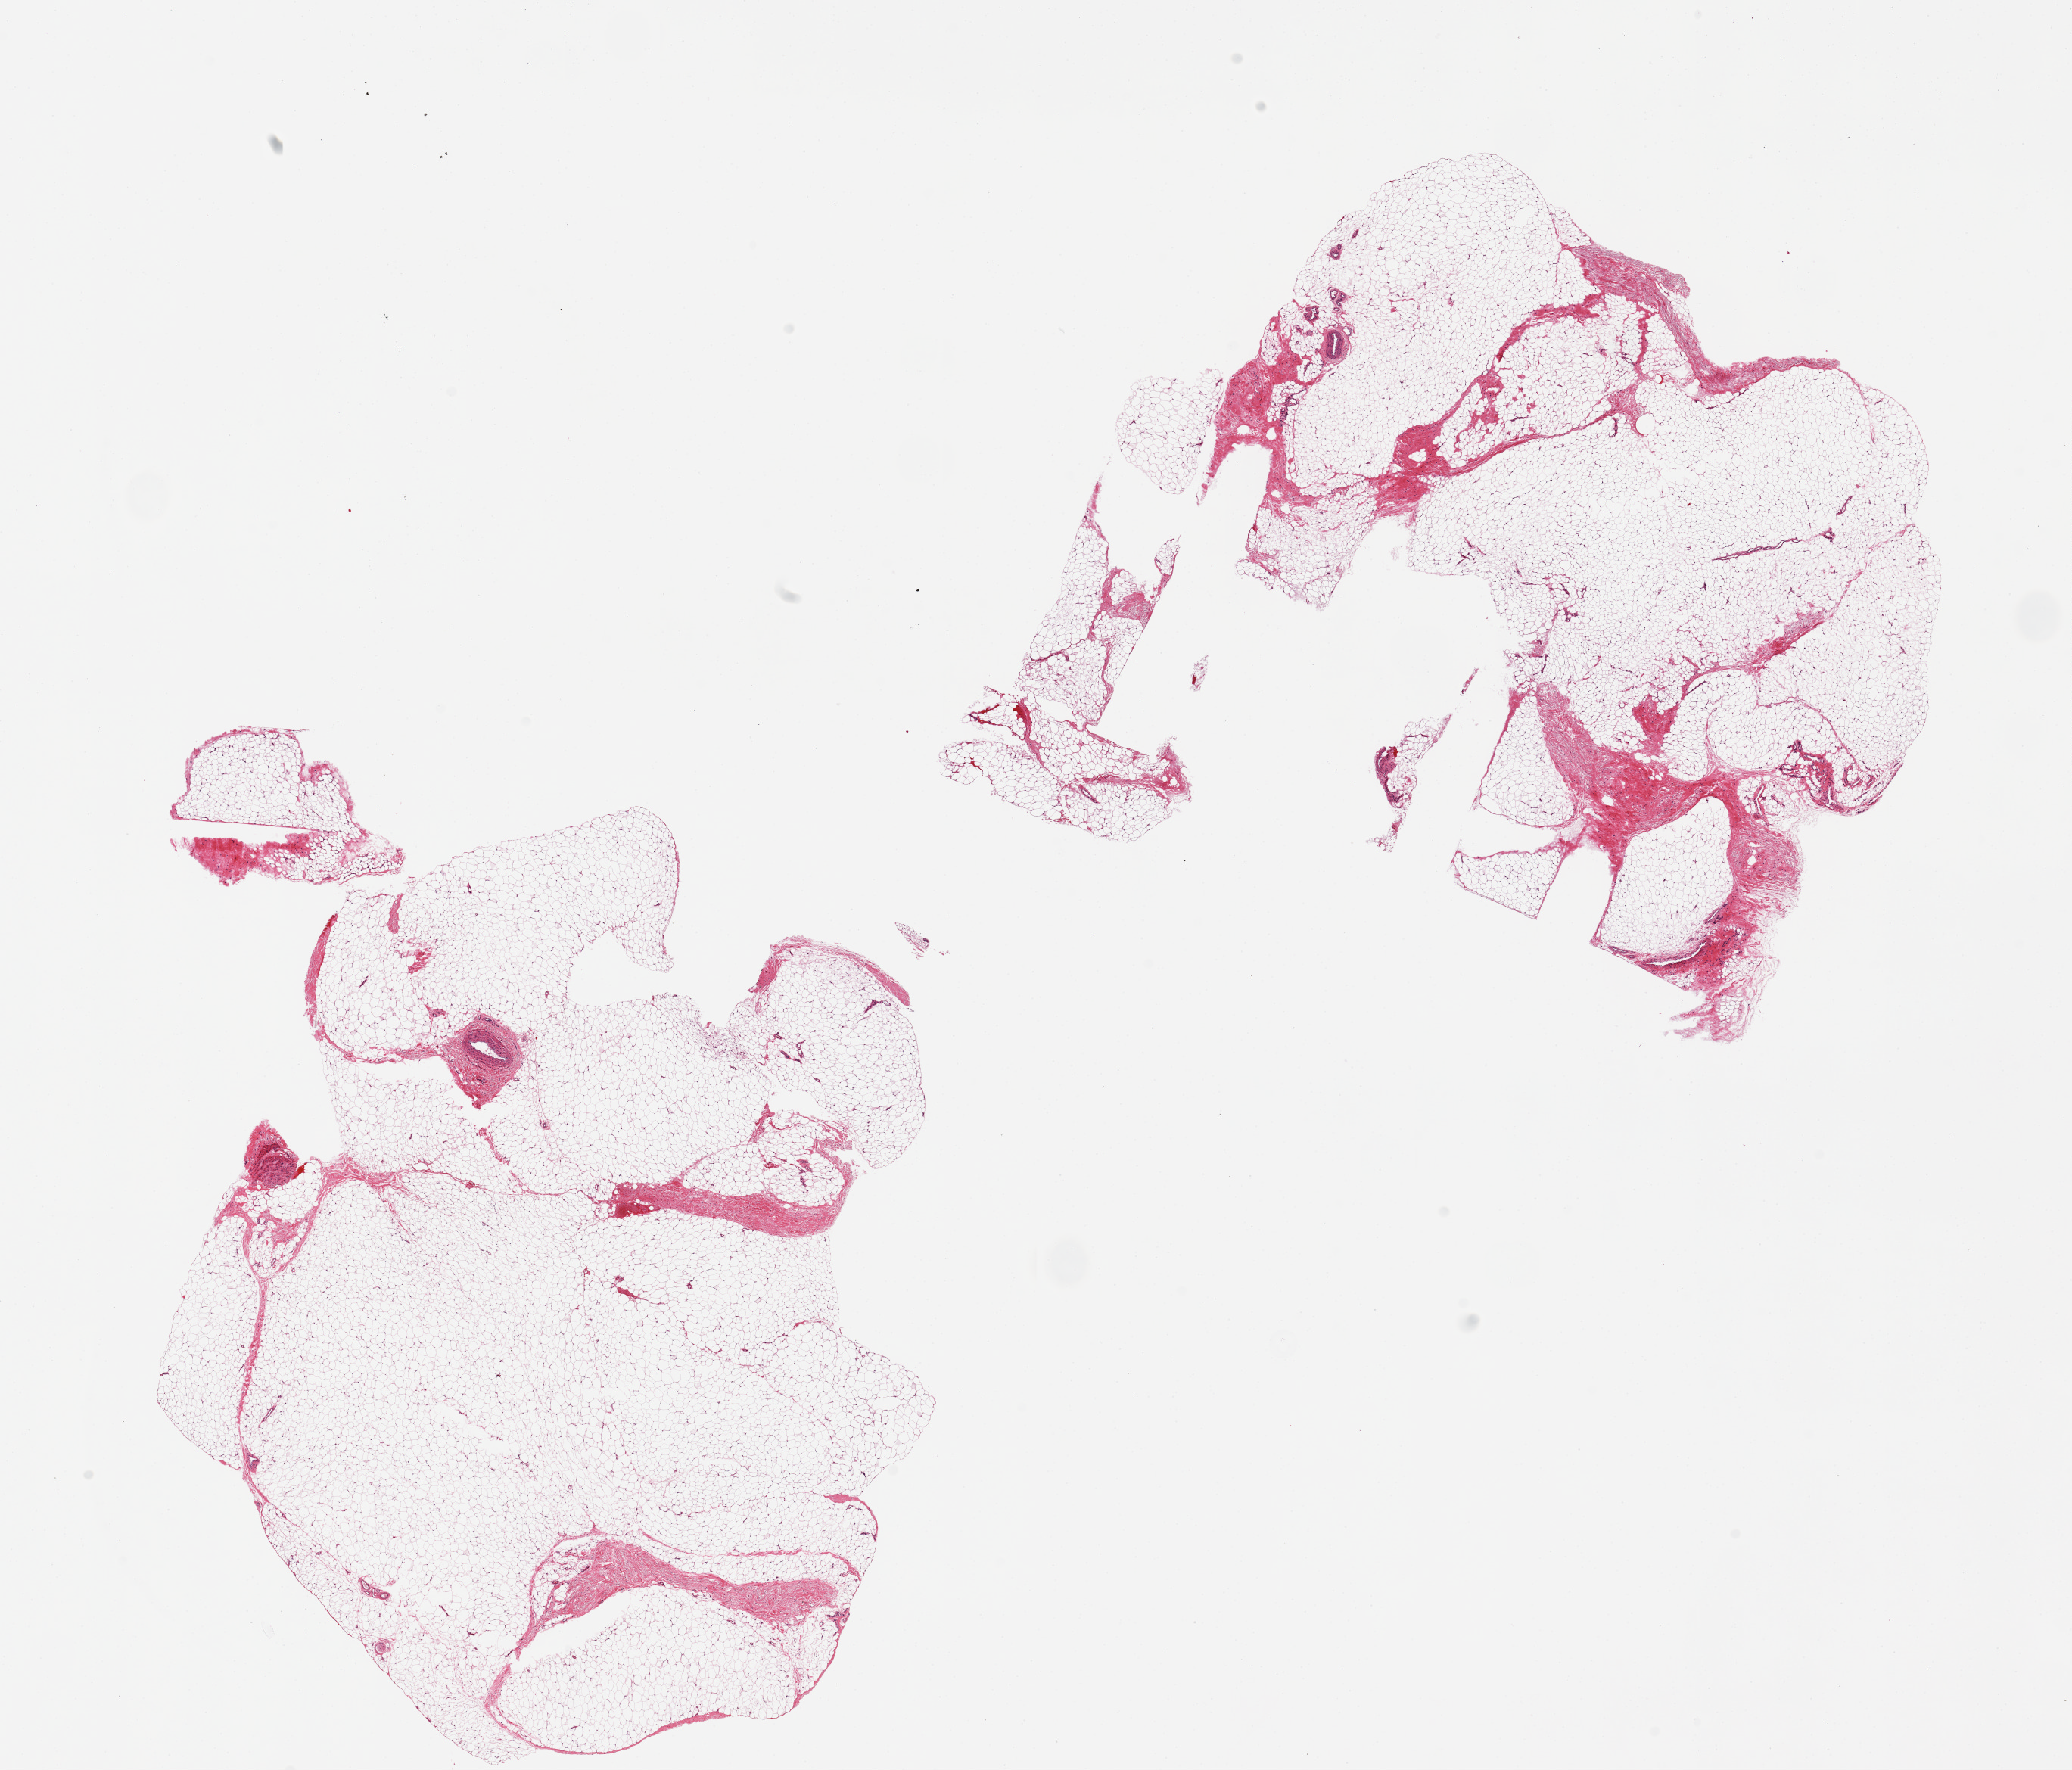
Digitized hematoxylin and eosin (H&E)-stained section, brightfield, whole scanned area (about 21.7 x 18.5 mm) shown as a low-resolution overview; PAXgene-fixed paraffin-embedded (PFPE) section; section of adipose tissue (target tissue); donor tissue sample.
Pathologist's review note for this sample: 2 pieces, 11.5x9 & 9x8.5mm. Well fixed, no artifacts.